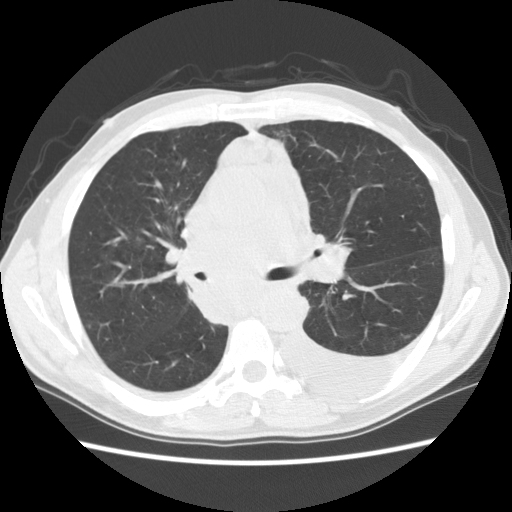
Chest CT (low-dose screening protocol), one axial image; baseline annual screen; lung window (W 1500 / L -600 HU); 2.5 mm slice thickness; standard (soft-tissue) reconstruction kernel (STANDARD); 140 kVp; 512 × 512 image matrix, field of view 346 × 346 mm. Male, age 60 years at enrolment. Current smoker at enrolment.
Expert reader's lesion annotation, bounding box (x1, y1, x2, y2) in pixels: (177, 237, 296, 327). No non-calcified nodule or mass ≥4 mm was recorded by the screening reader at this exam. Official screen result: negative screen, significant abnormalities not suspicious for lung cancer. Participant outcome: lung cancer diagnosed 12 days after this screen — squamous cell carcinoma, NOS, carina, poorly differentiated (G3), stage IV (AJCC 6th edition).